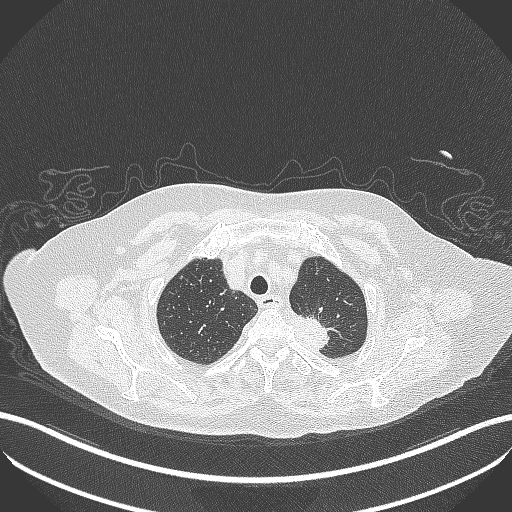
Chest CT, one axial slice; slice 291 of 353 in the series (ordered by position); lung window (W 1500 / L -600 HU); 512 × 512 image matrix, field of view 400 × 400 mm. Female patient, age 81 years. From the clinical record (not read from this slice): clinical TNM (as recorded): T2a N0 M0.
Outlined on this slice (bounding box drawn by a radiologist):
- lung tumour (recorded histology: adenocarcinoma): box from (x=284, y=311) to (x=335, y=360) px